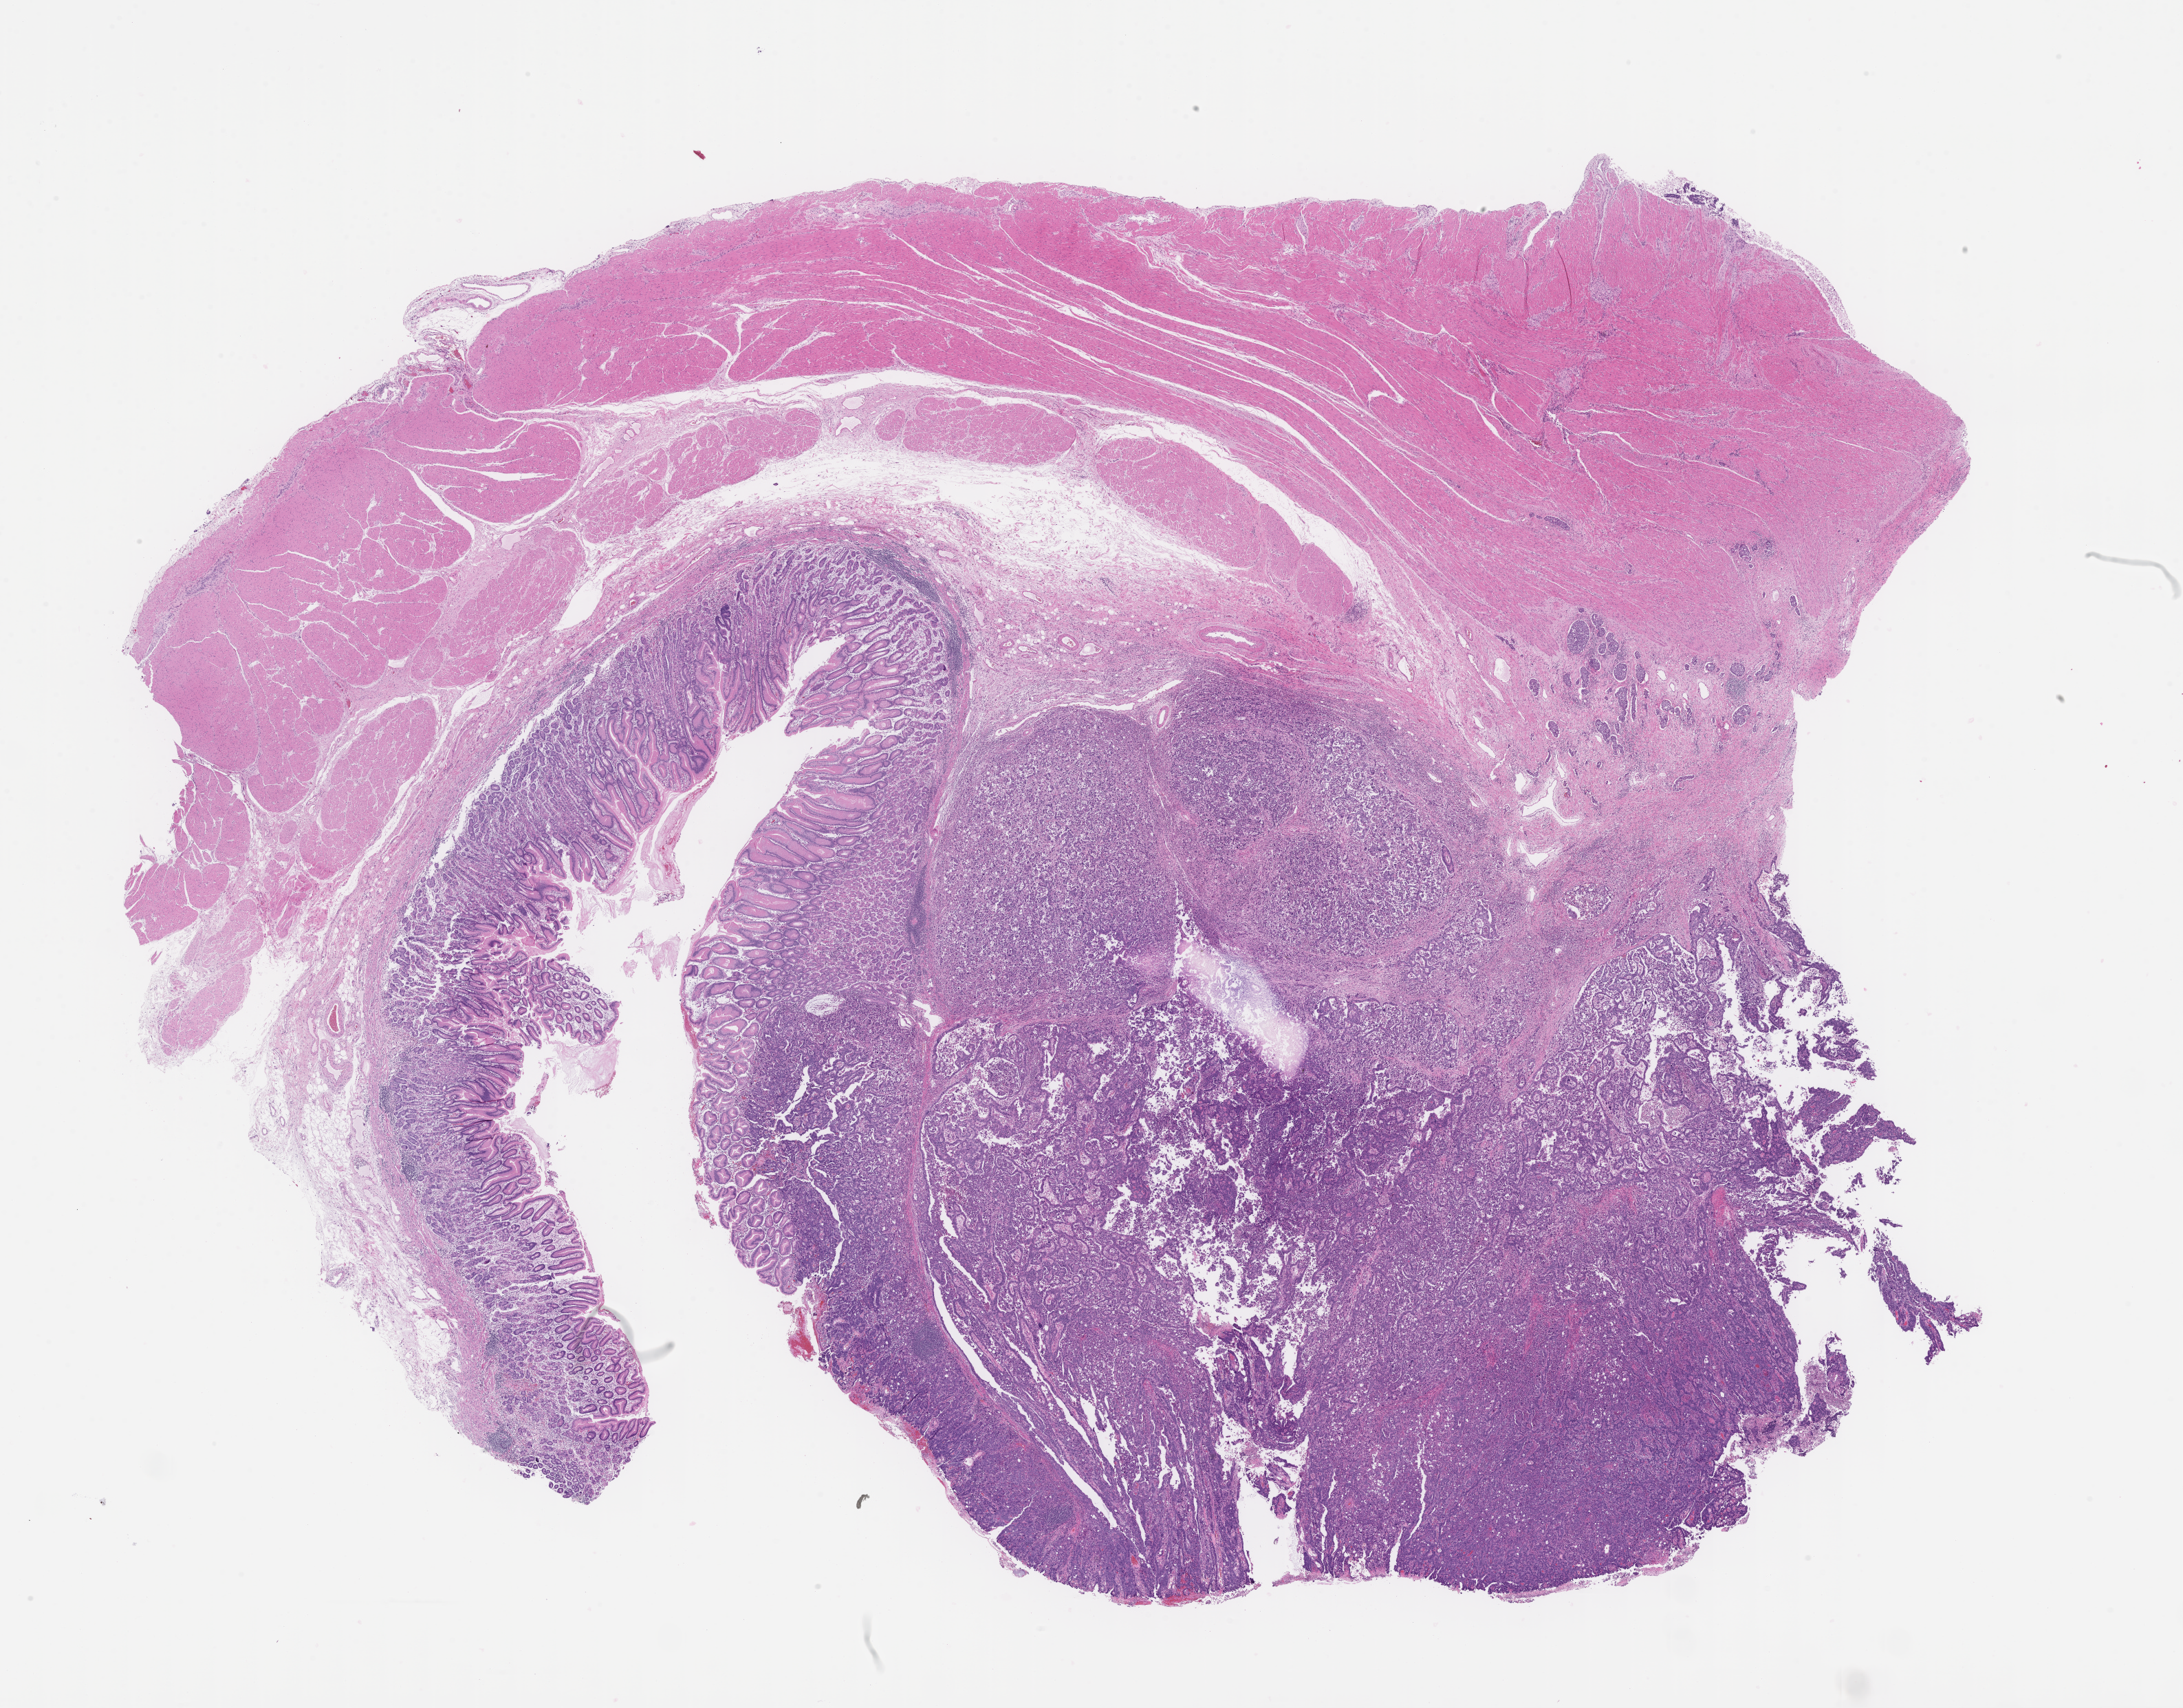
Digitized H&E-stained section — shown as a low-resolution overview of the whole scanned area (about 25.6 x 20.1 mm), formalin-fixed paraffin-embedded section, site: esophagus, specimen time point: archival tissue. Female patient.
• this section: primary tumor
• diagnosis: Gastric Carcinoma